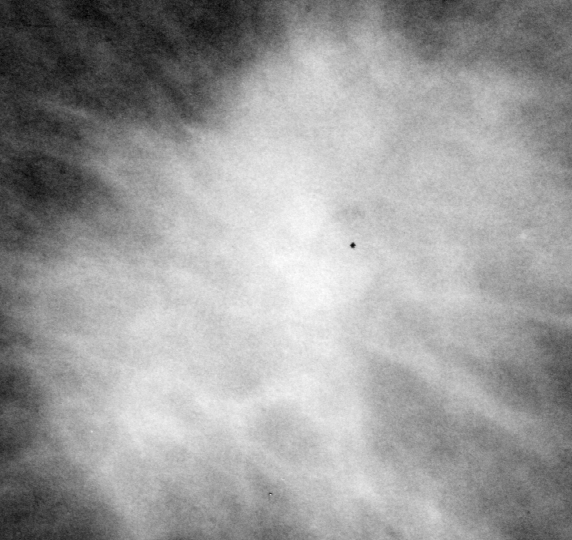
Region of interest cut from a scanned film mammogram (one marked finding); left breast; MLO view; BI-RADS breast density category 2 (scale 1–4).
Marked abnormality: mass, shape irregular, margins spiculated; BI-RADS assessment category 5; pathology result (as recorded, not read from the image): malignant.